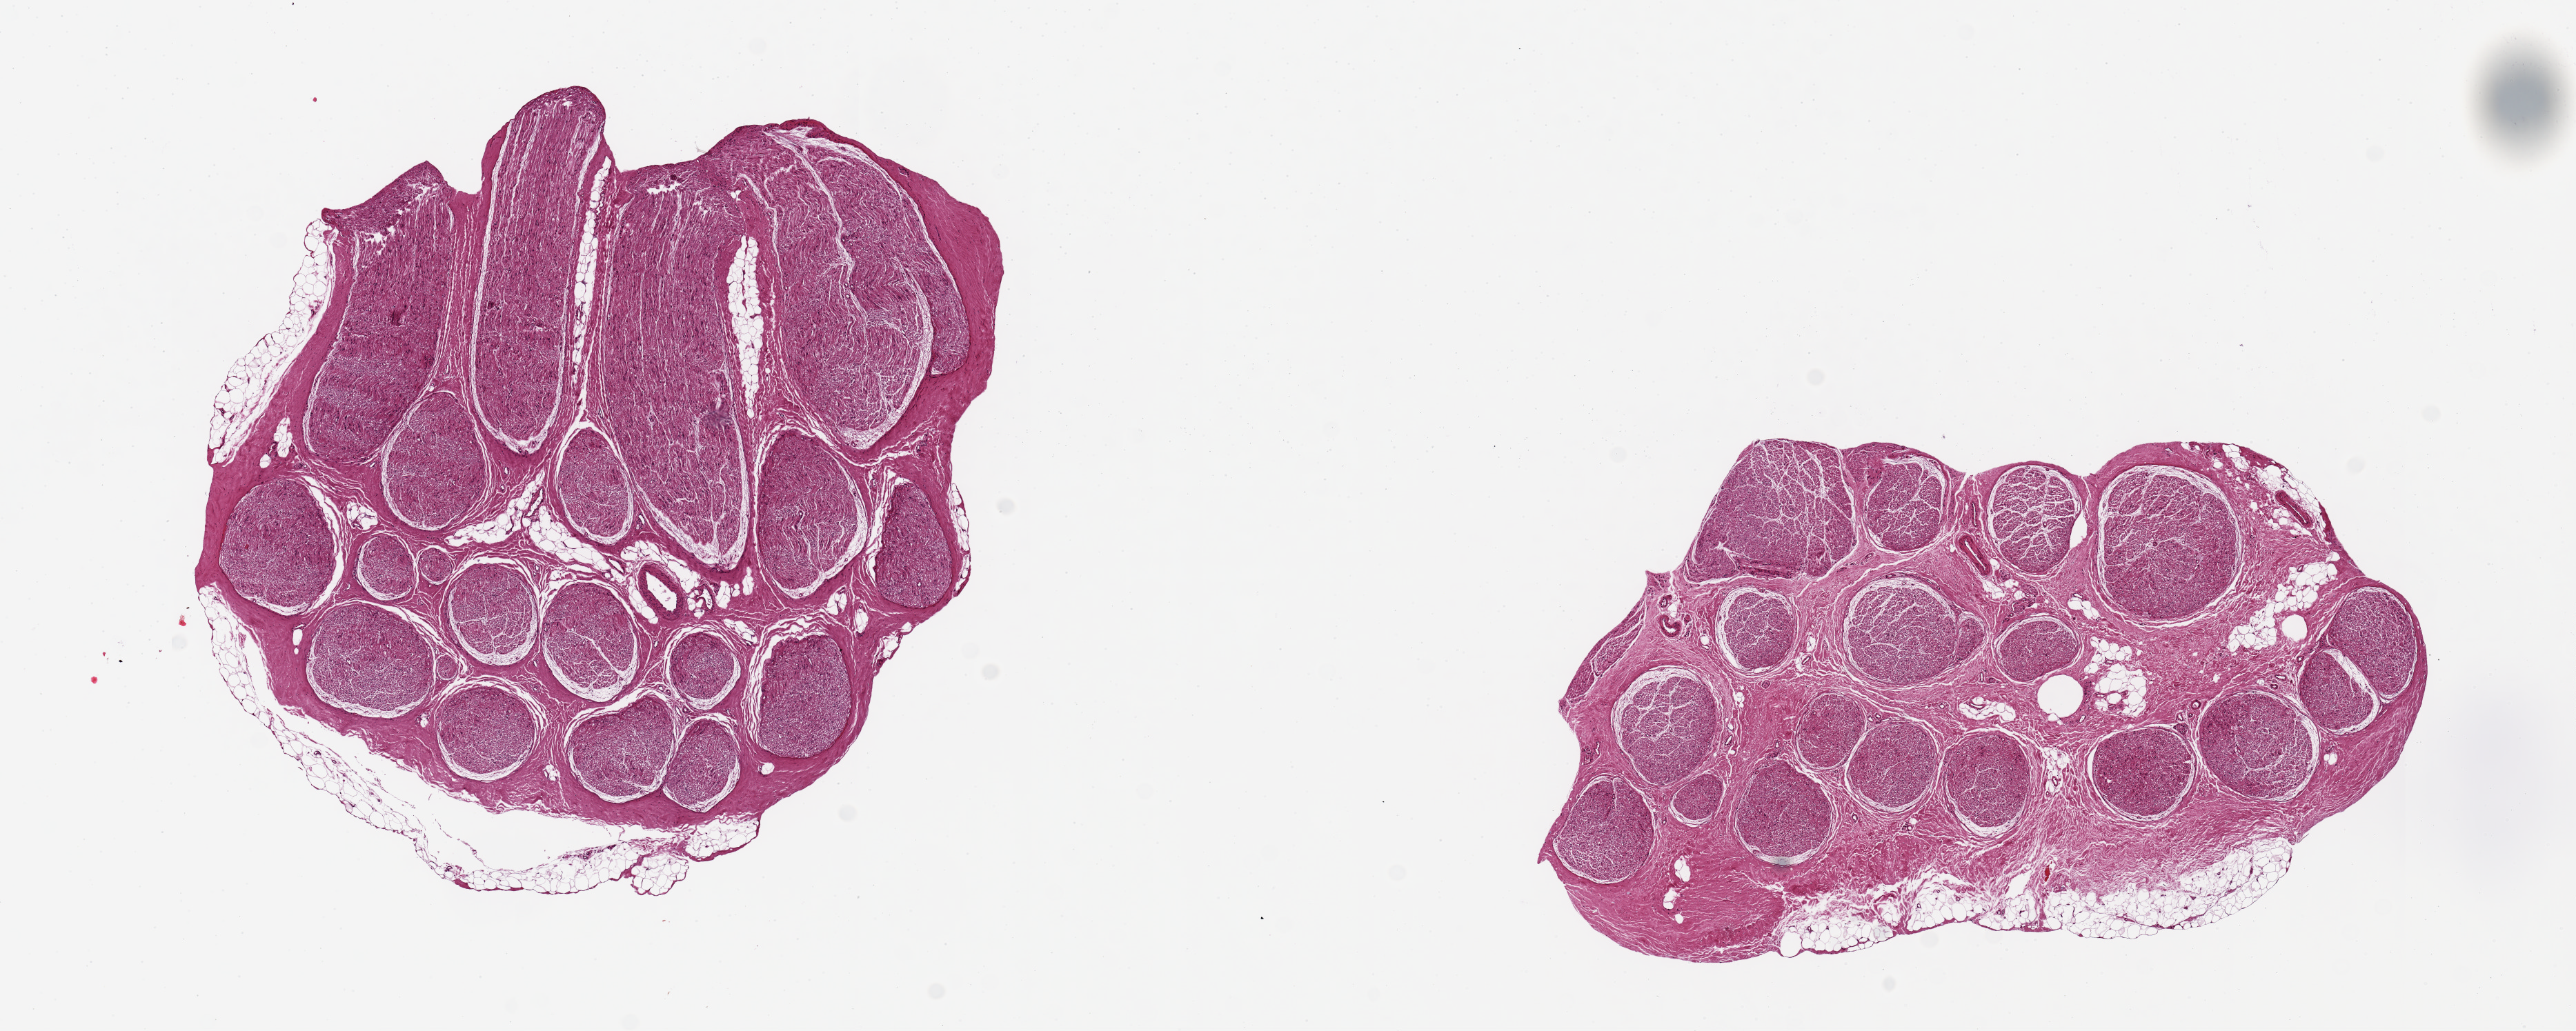
H&E whole-slide image — a low-resolution overview of the entire scanned area, about 14.8 x 5.9 mm, PAXgene-fixed paraffin-embedded (PFPE) section, section of tibial nerve (target tissue), donor tissue sample. Male donor.
Review note (as recorded): 2 ~4x3.5mm pieces, relatively clean.